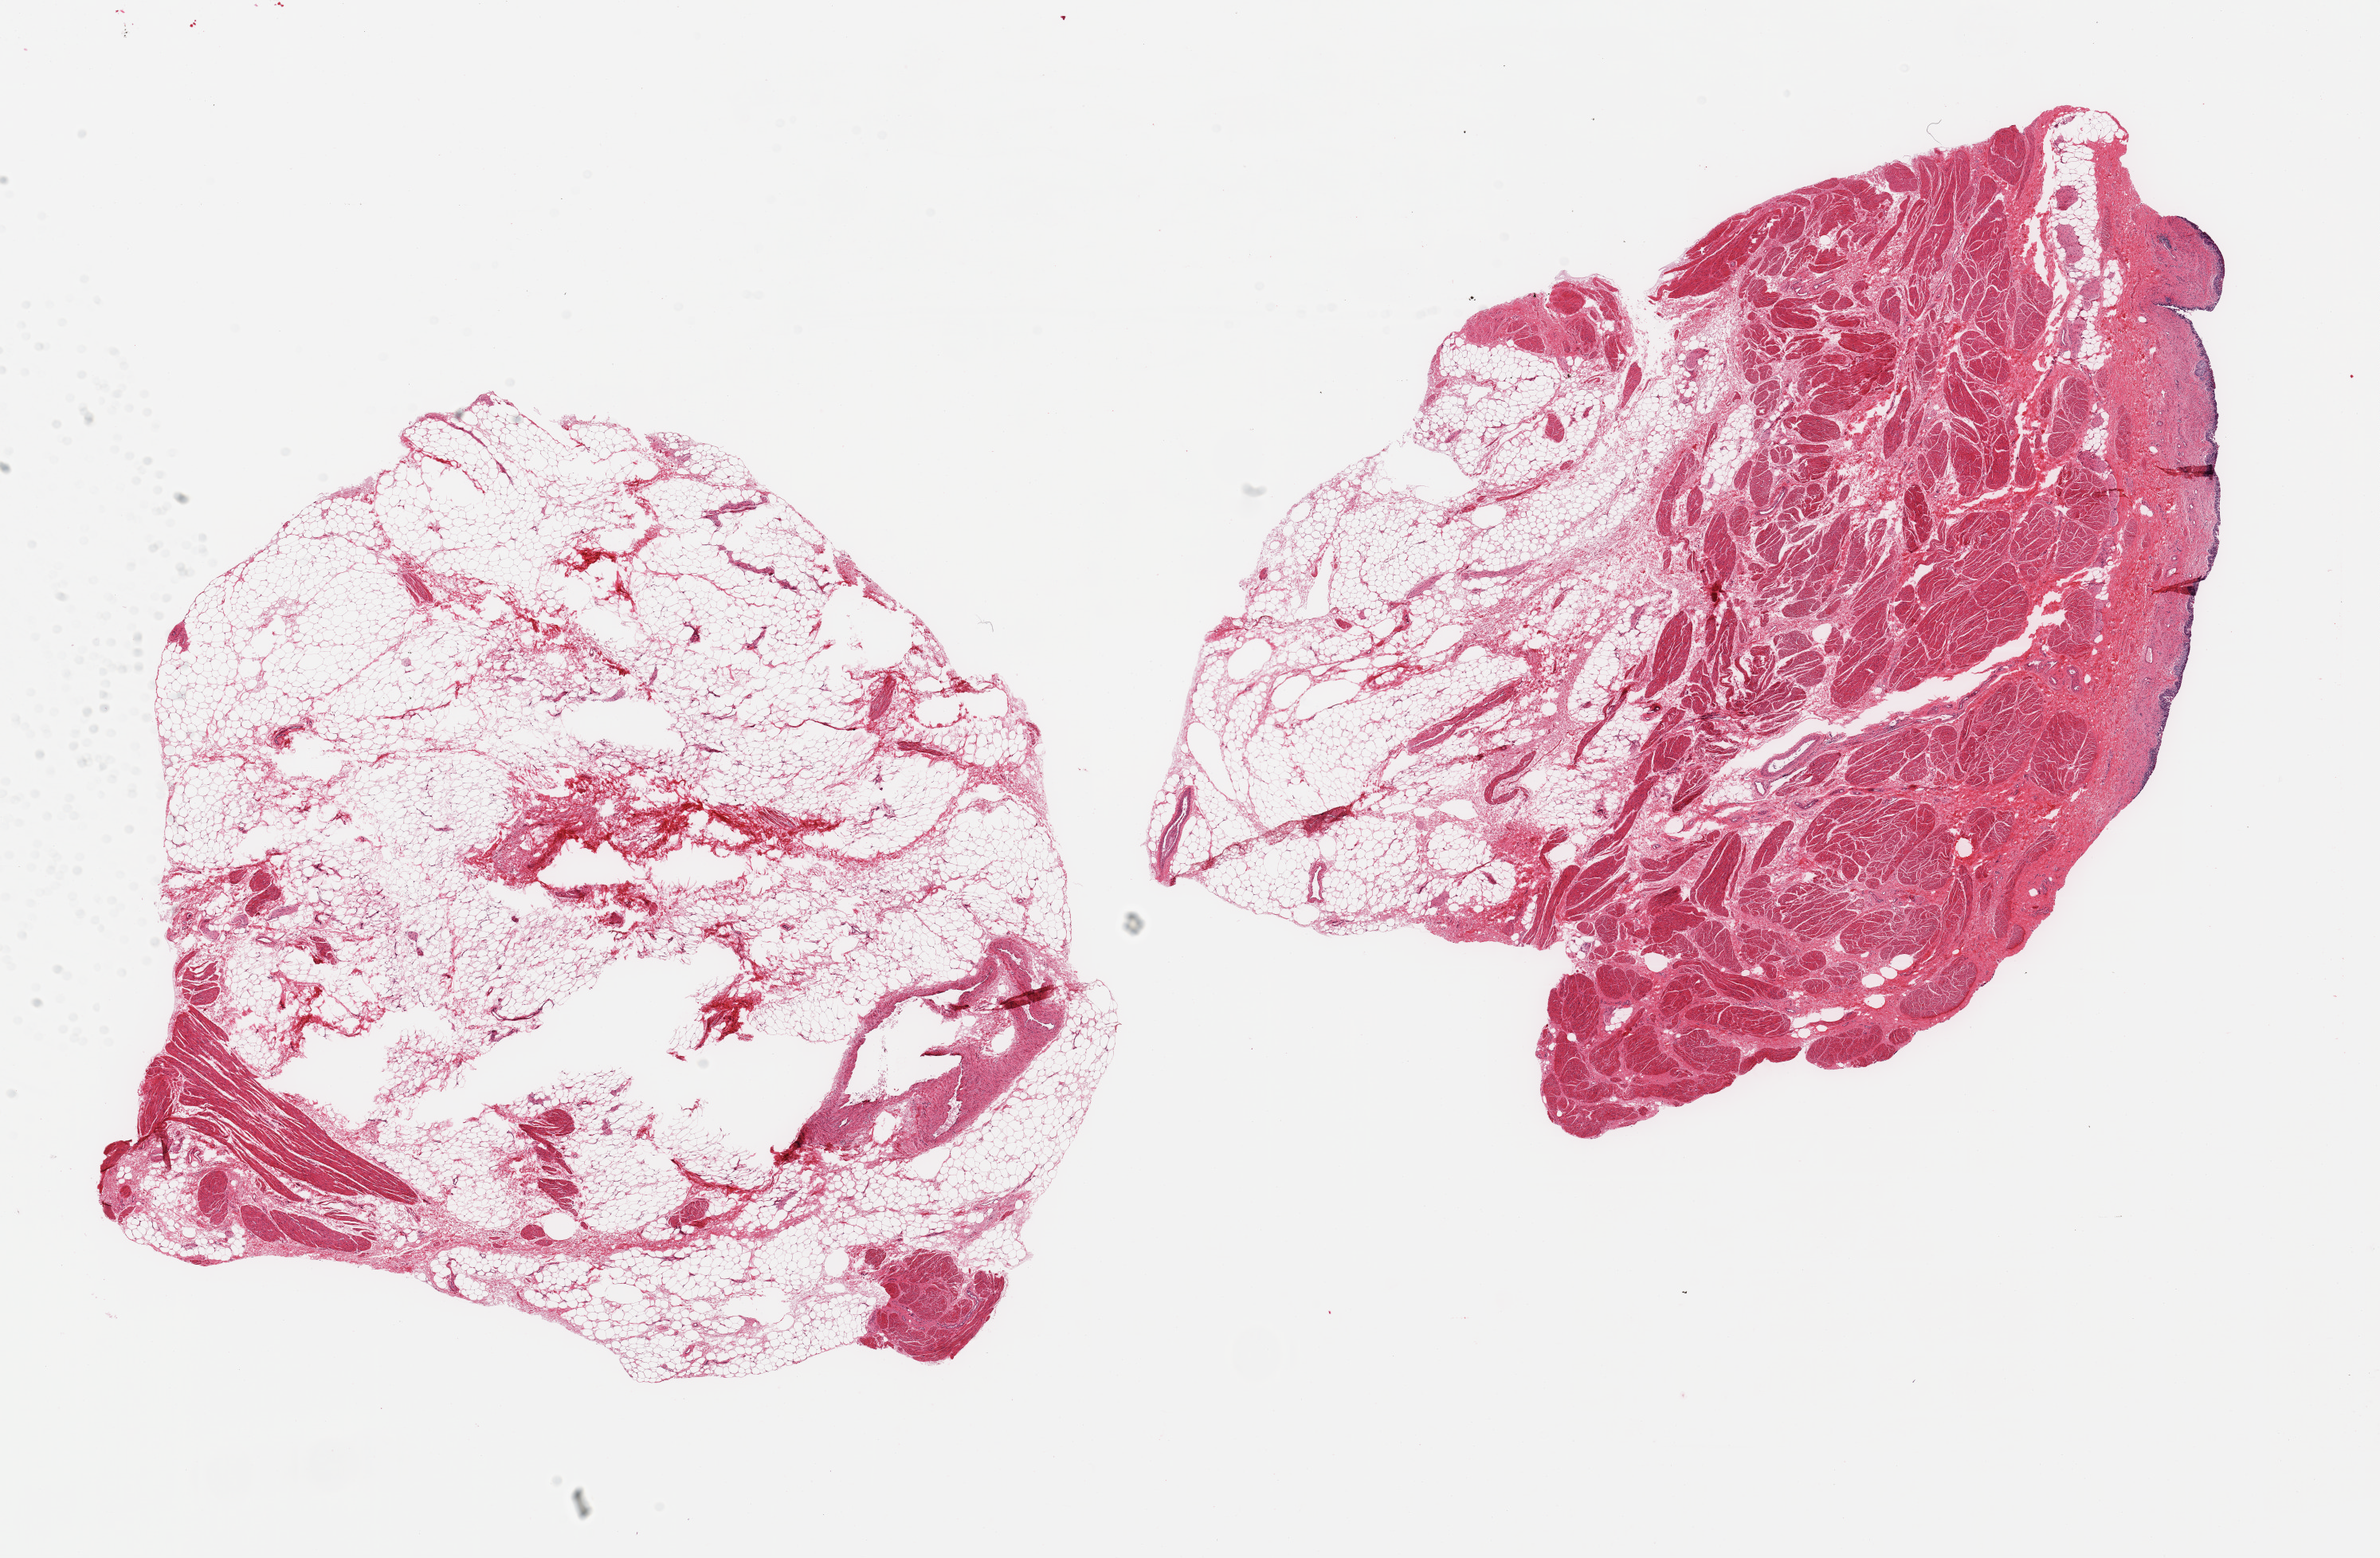
Digitized haematoxylin and eosin-stained section — shown as a low-resolution overview of the whole scanned area (about 23.6 x 15.5 mm). PAXgene-fixed, paraffin-embedded tissue. Section of uterus (target tissue). Tissue donor sample.
- reviewer comment on this tissue sample: 2 pieces; not uterus; looks like bladder and fat tissue